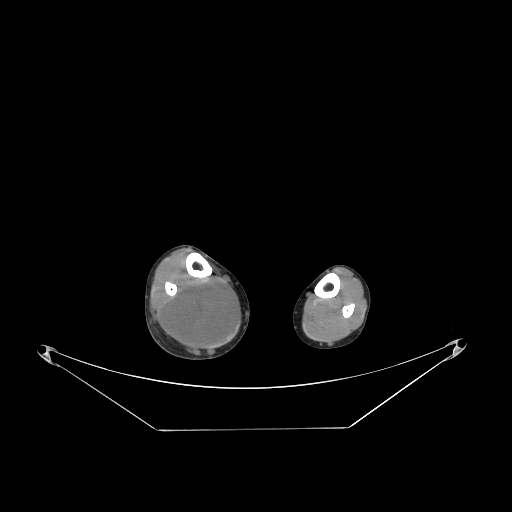
CT of an extremity soft-tissue mass (from a PET/CT study), one axial slice; position 78 of 267 along the scan axis; soft-tissue window (W 400 / L 40 HU); 3.75 mm slice thickness; 512 × 512 image matrix, field of view 500 × 500 mm. Male patient. From the clinical record (not read from this slice): histological type: liposarcoma - round cell; grade: high; site of the primary tumour: right calf.
Outlined on this slice (expert contour drawn on MRI and transferred to this co-registered scan by the dataset authors):
- gross tumour volume (mass): box from (x=164, y=279) to (x=239, y=348) px